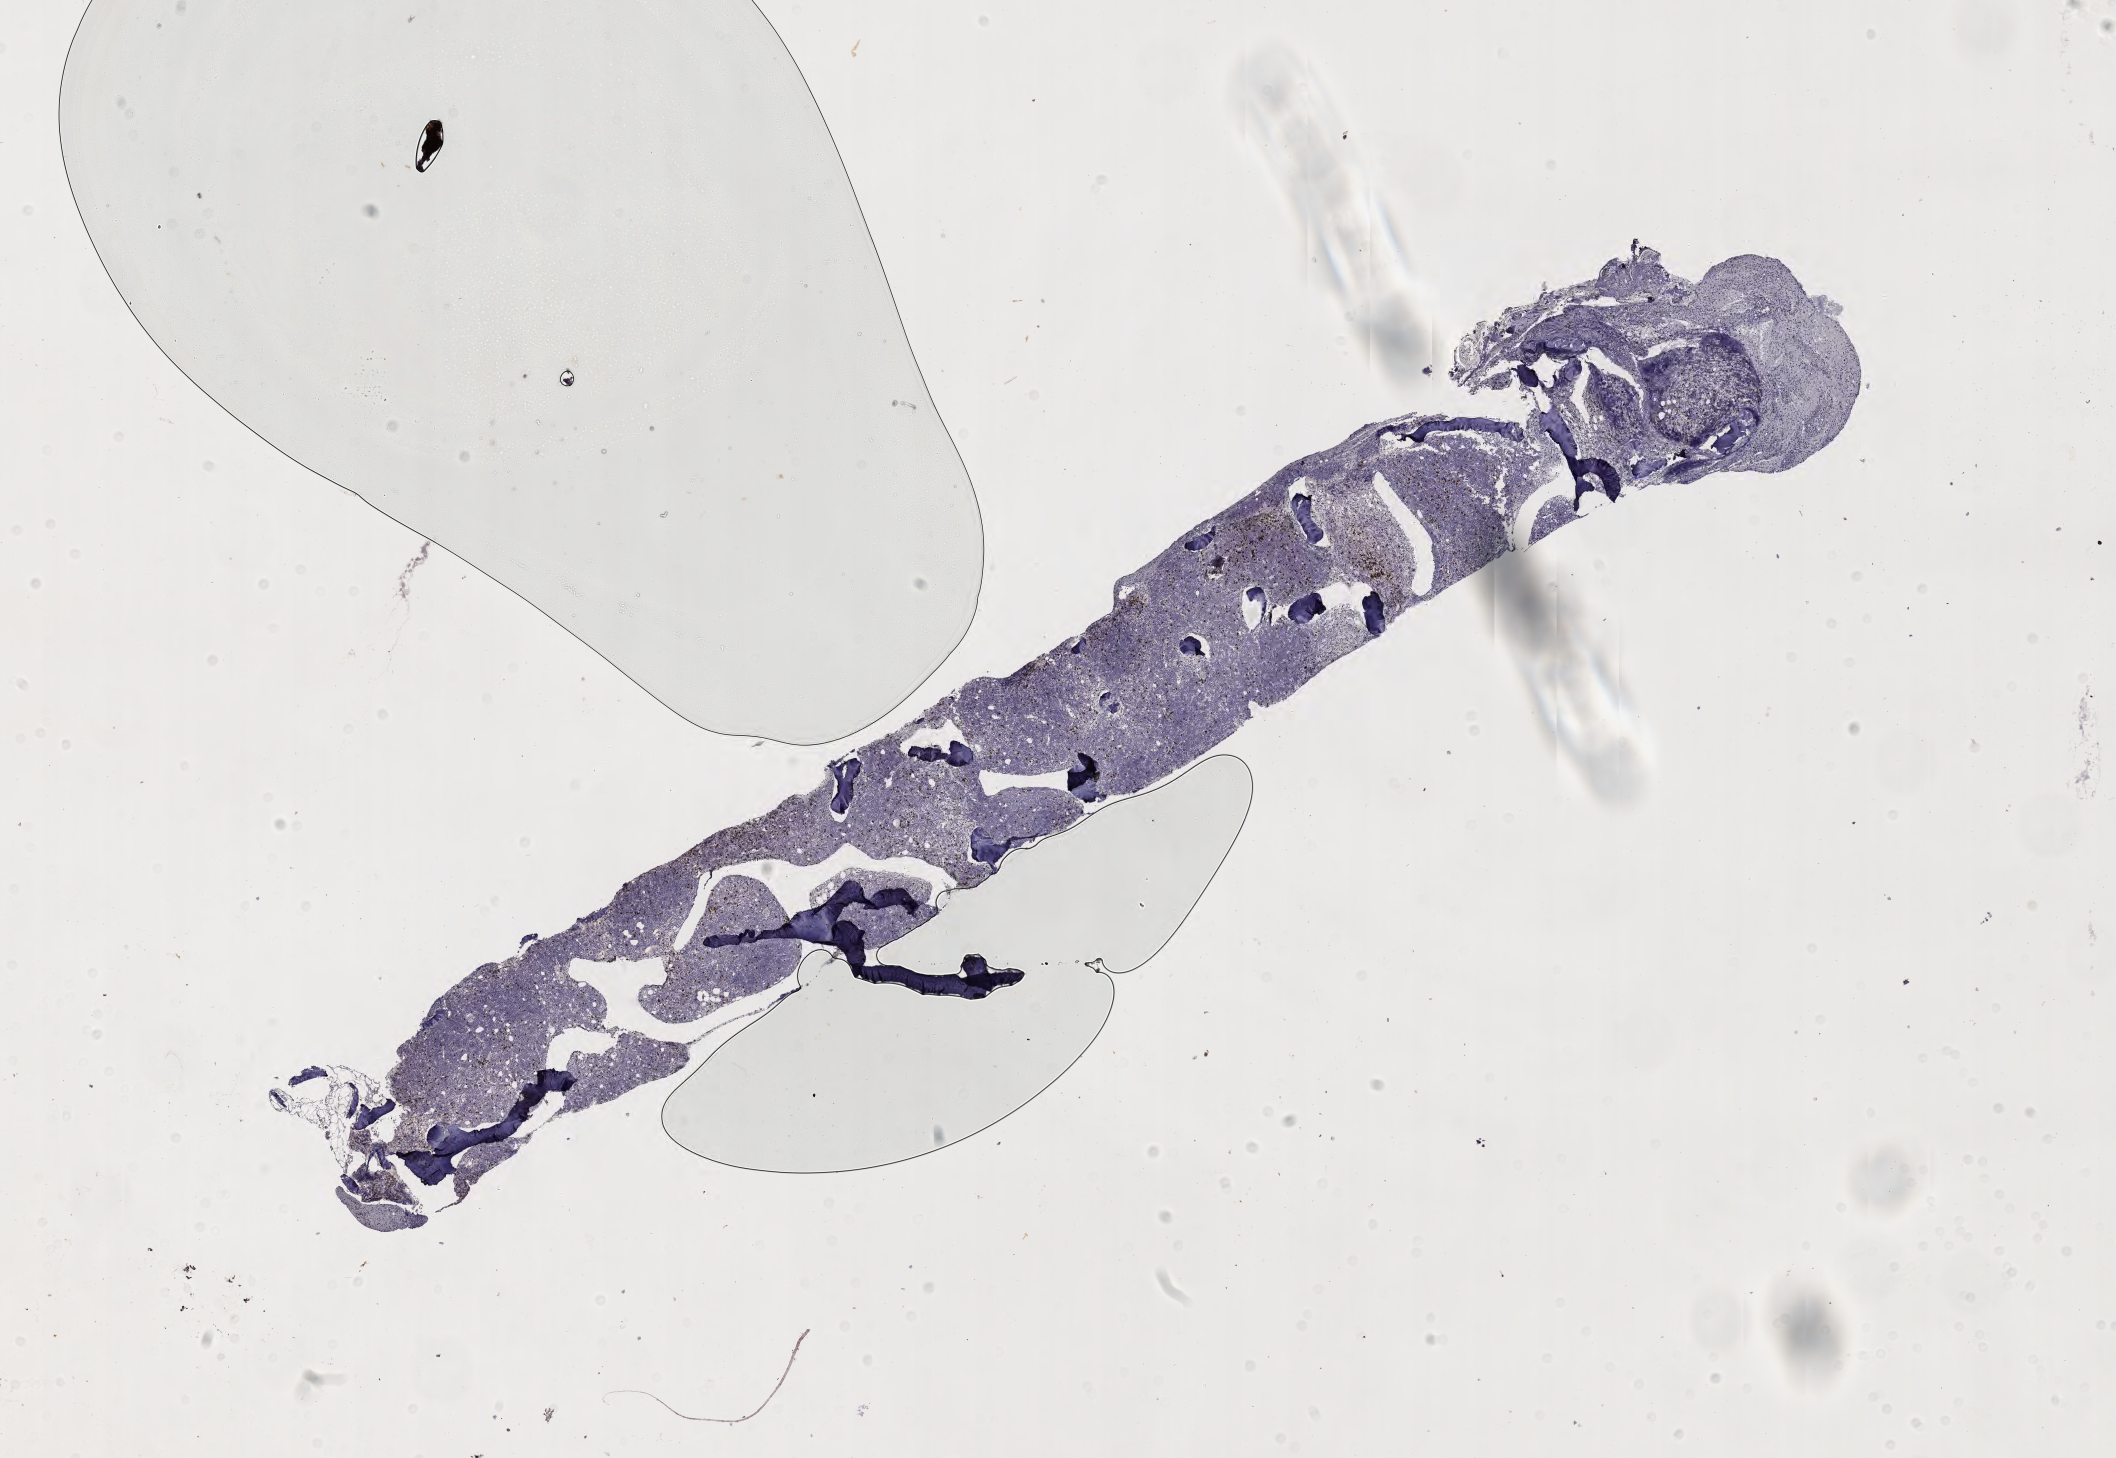
Whole-slide image, immunohistochemical stain for CD5, shown as a low-resolution overview of the whole scanned area (about 17.1 x 11.8 mm). Tumor tissue. Patient female; 64 years old.
Diagnosis: Burkitt lymphoma, NOS.